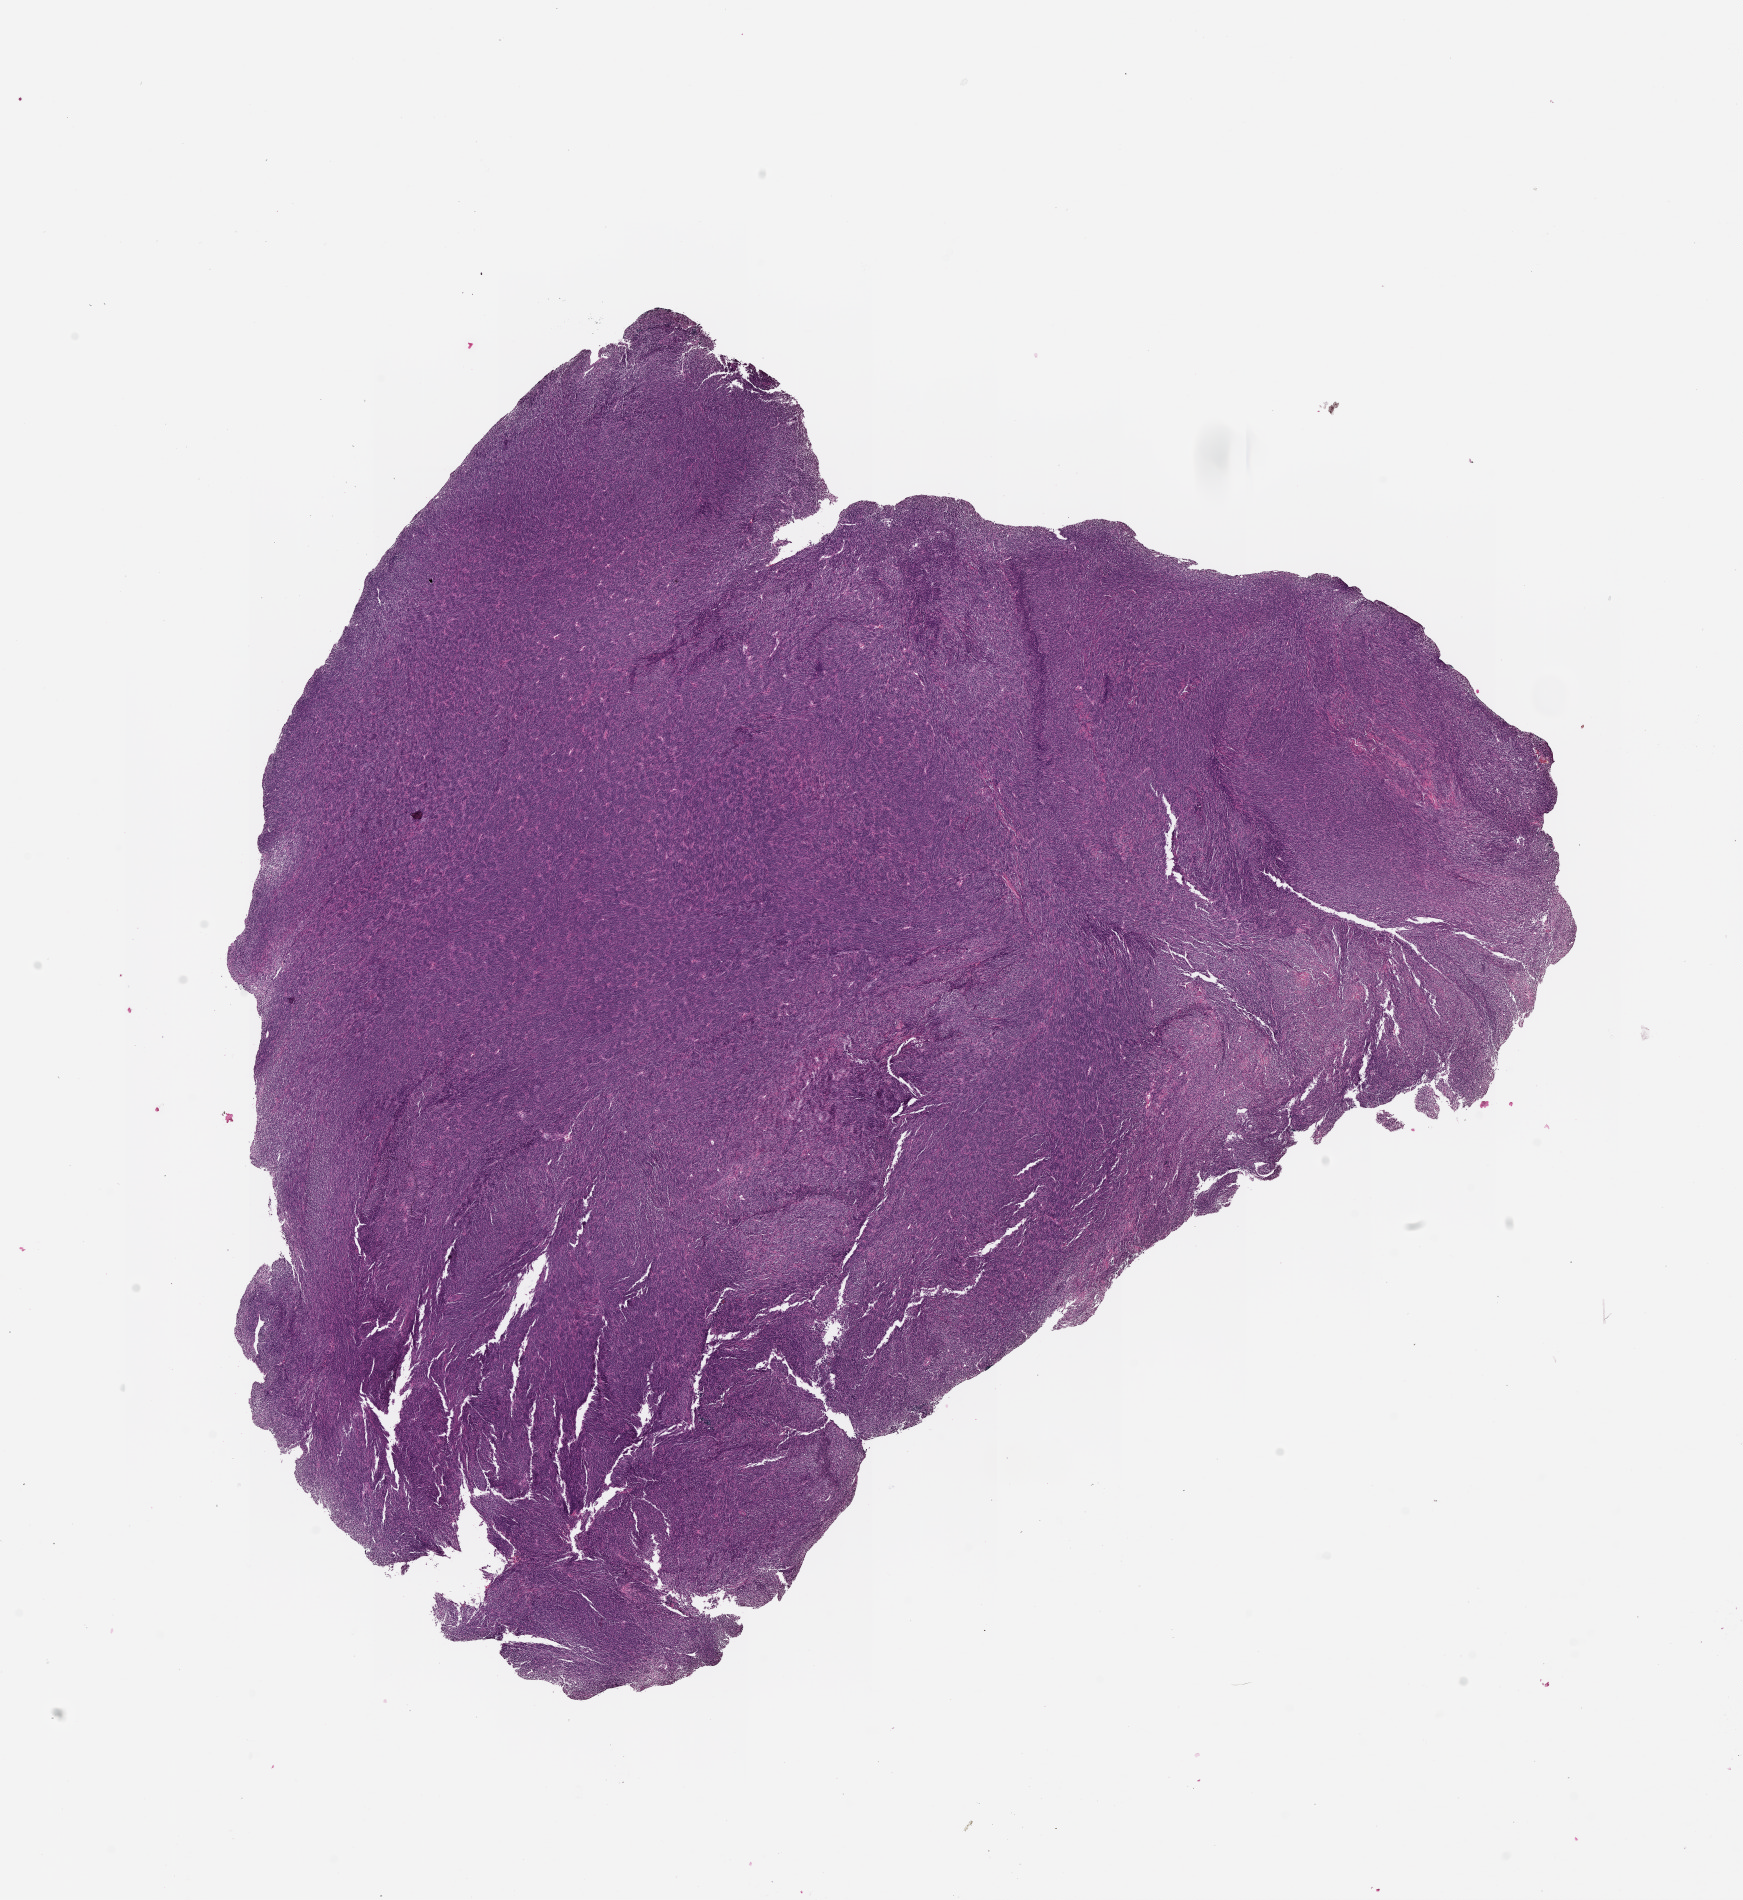
H&E-stained whole-slide image, whole scanned area (about 14.0 x 15.3 mm, slide scanned at 20x) shown as a low-resolution overview.
Patient diagnosis (cohort enrolment): sarcoma (site not recorded at cohort level).